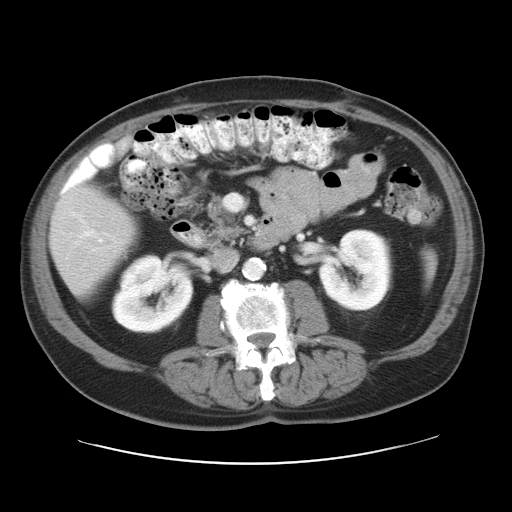
Contrast-enhanced abdominal CT, one axial slice; 120 kVp; intravenous contrast given; soft-tissue window (W 400 / L 40 HU); 7.5 mm slice thickness; 512 × 512 image matrix. Male patient, age 74 years. From the clinical record (not read from this slice): diagnosis: colorectal cancer liver metastases, imaged before liver resection; multiple liver metastases: no; largest metastasis: 5 cm.
Outlined on this slice (expert manual segmentation):
- hepatic veins: bounding box (x1, y1, x2, y2) in pixels: (99, 239, 102, 242)
- liver: (51, 188, 134, 292)
- planned liver remnant (the part of the liver to remain after resection): (51, 188, 134, 293)